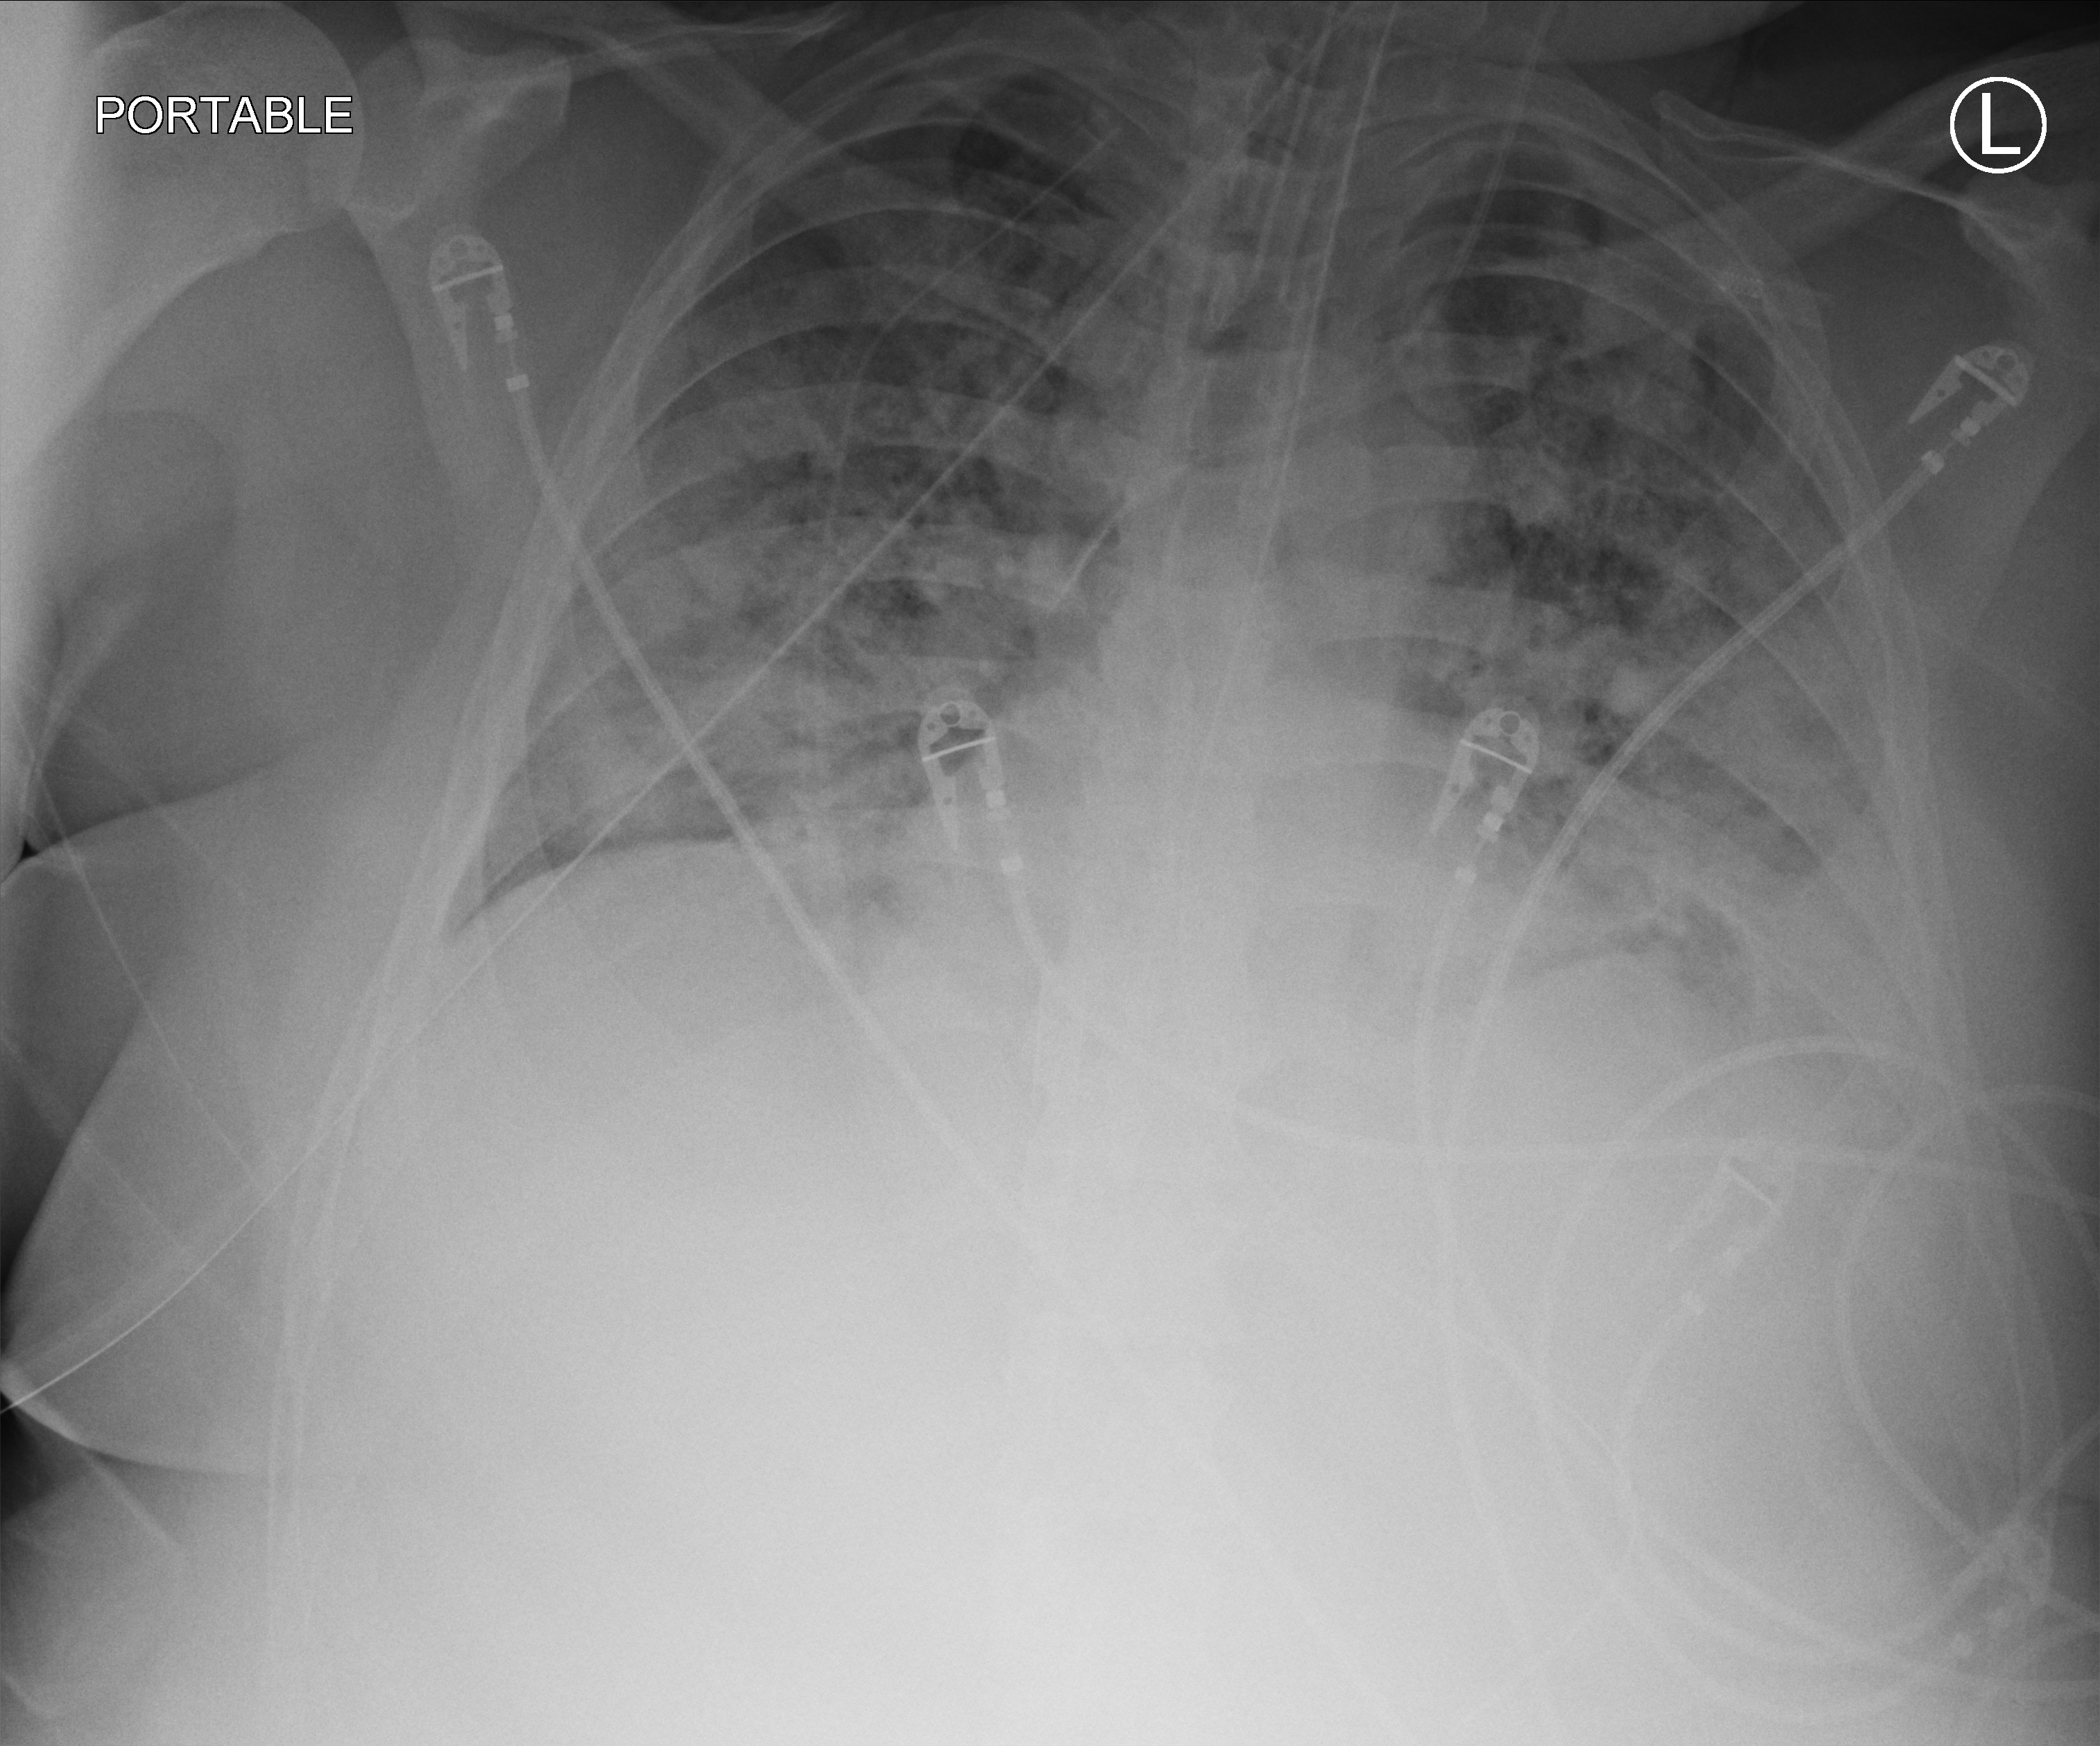
Chest X-ray (portable), anteroposterior (AP) projection. Adult patient hospitalised with COVID-19, age 18–59 years.
Admission-level facts for this patient (not findings on this image; timing relative to this image not recorded): chronic kidney disease (admission record): no; mechanically ventilated during this hospital stay: yes; length of hospital stay: 15 days.